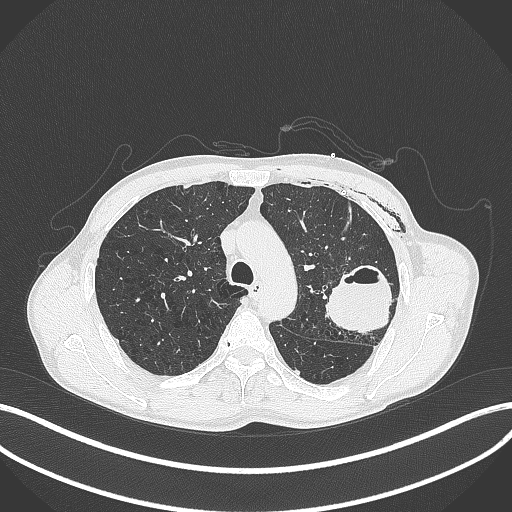
Chest CT, one axial slice. Slice 290 of 457 in the series (ordered by position). Reconstruction kernel B70f. 120 kVp. Lung window (W 1500 / L -600 HU). 1 mm slice thickness. 512 × 512 image matrix, field of view 400 × 400 mm. Patient: male, 58 years. Case-level facts recorded for this patient, not image findings: clinical TNM (as recorded): T3 N0 M0.
Structures marked on this image (bounding box drawn by a radiologist):
- lung tumour (recorded histology: adenocarcinoma): bounding box [x1, y1, x2, y2] px = [324, 262, 393, 335]